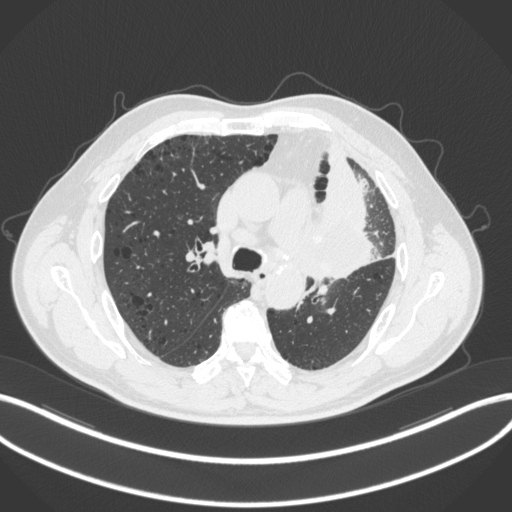
Chest CT, one axial slice; position 188 of 286 along the scan axis; reconstruction kernel B31f; 120 kVp; lung window (W 1500 / L -600 HU); 512 × 512 image matrix, field of view 400 × 400 mm. Male patient, age 68 years. Case-level facts recorded for this patient, not image findings: clinical TNM (as recorded): T3 N3 M1.
Structures marked on this image (bounding box drawn by a radiologist):
- lung tumour (recorded histology: adenocarcinoma): box from (x=301, y=203) to (x=382, y=289) px